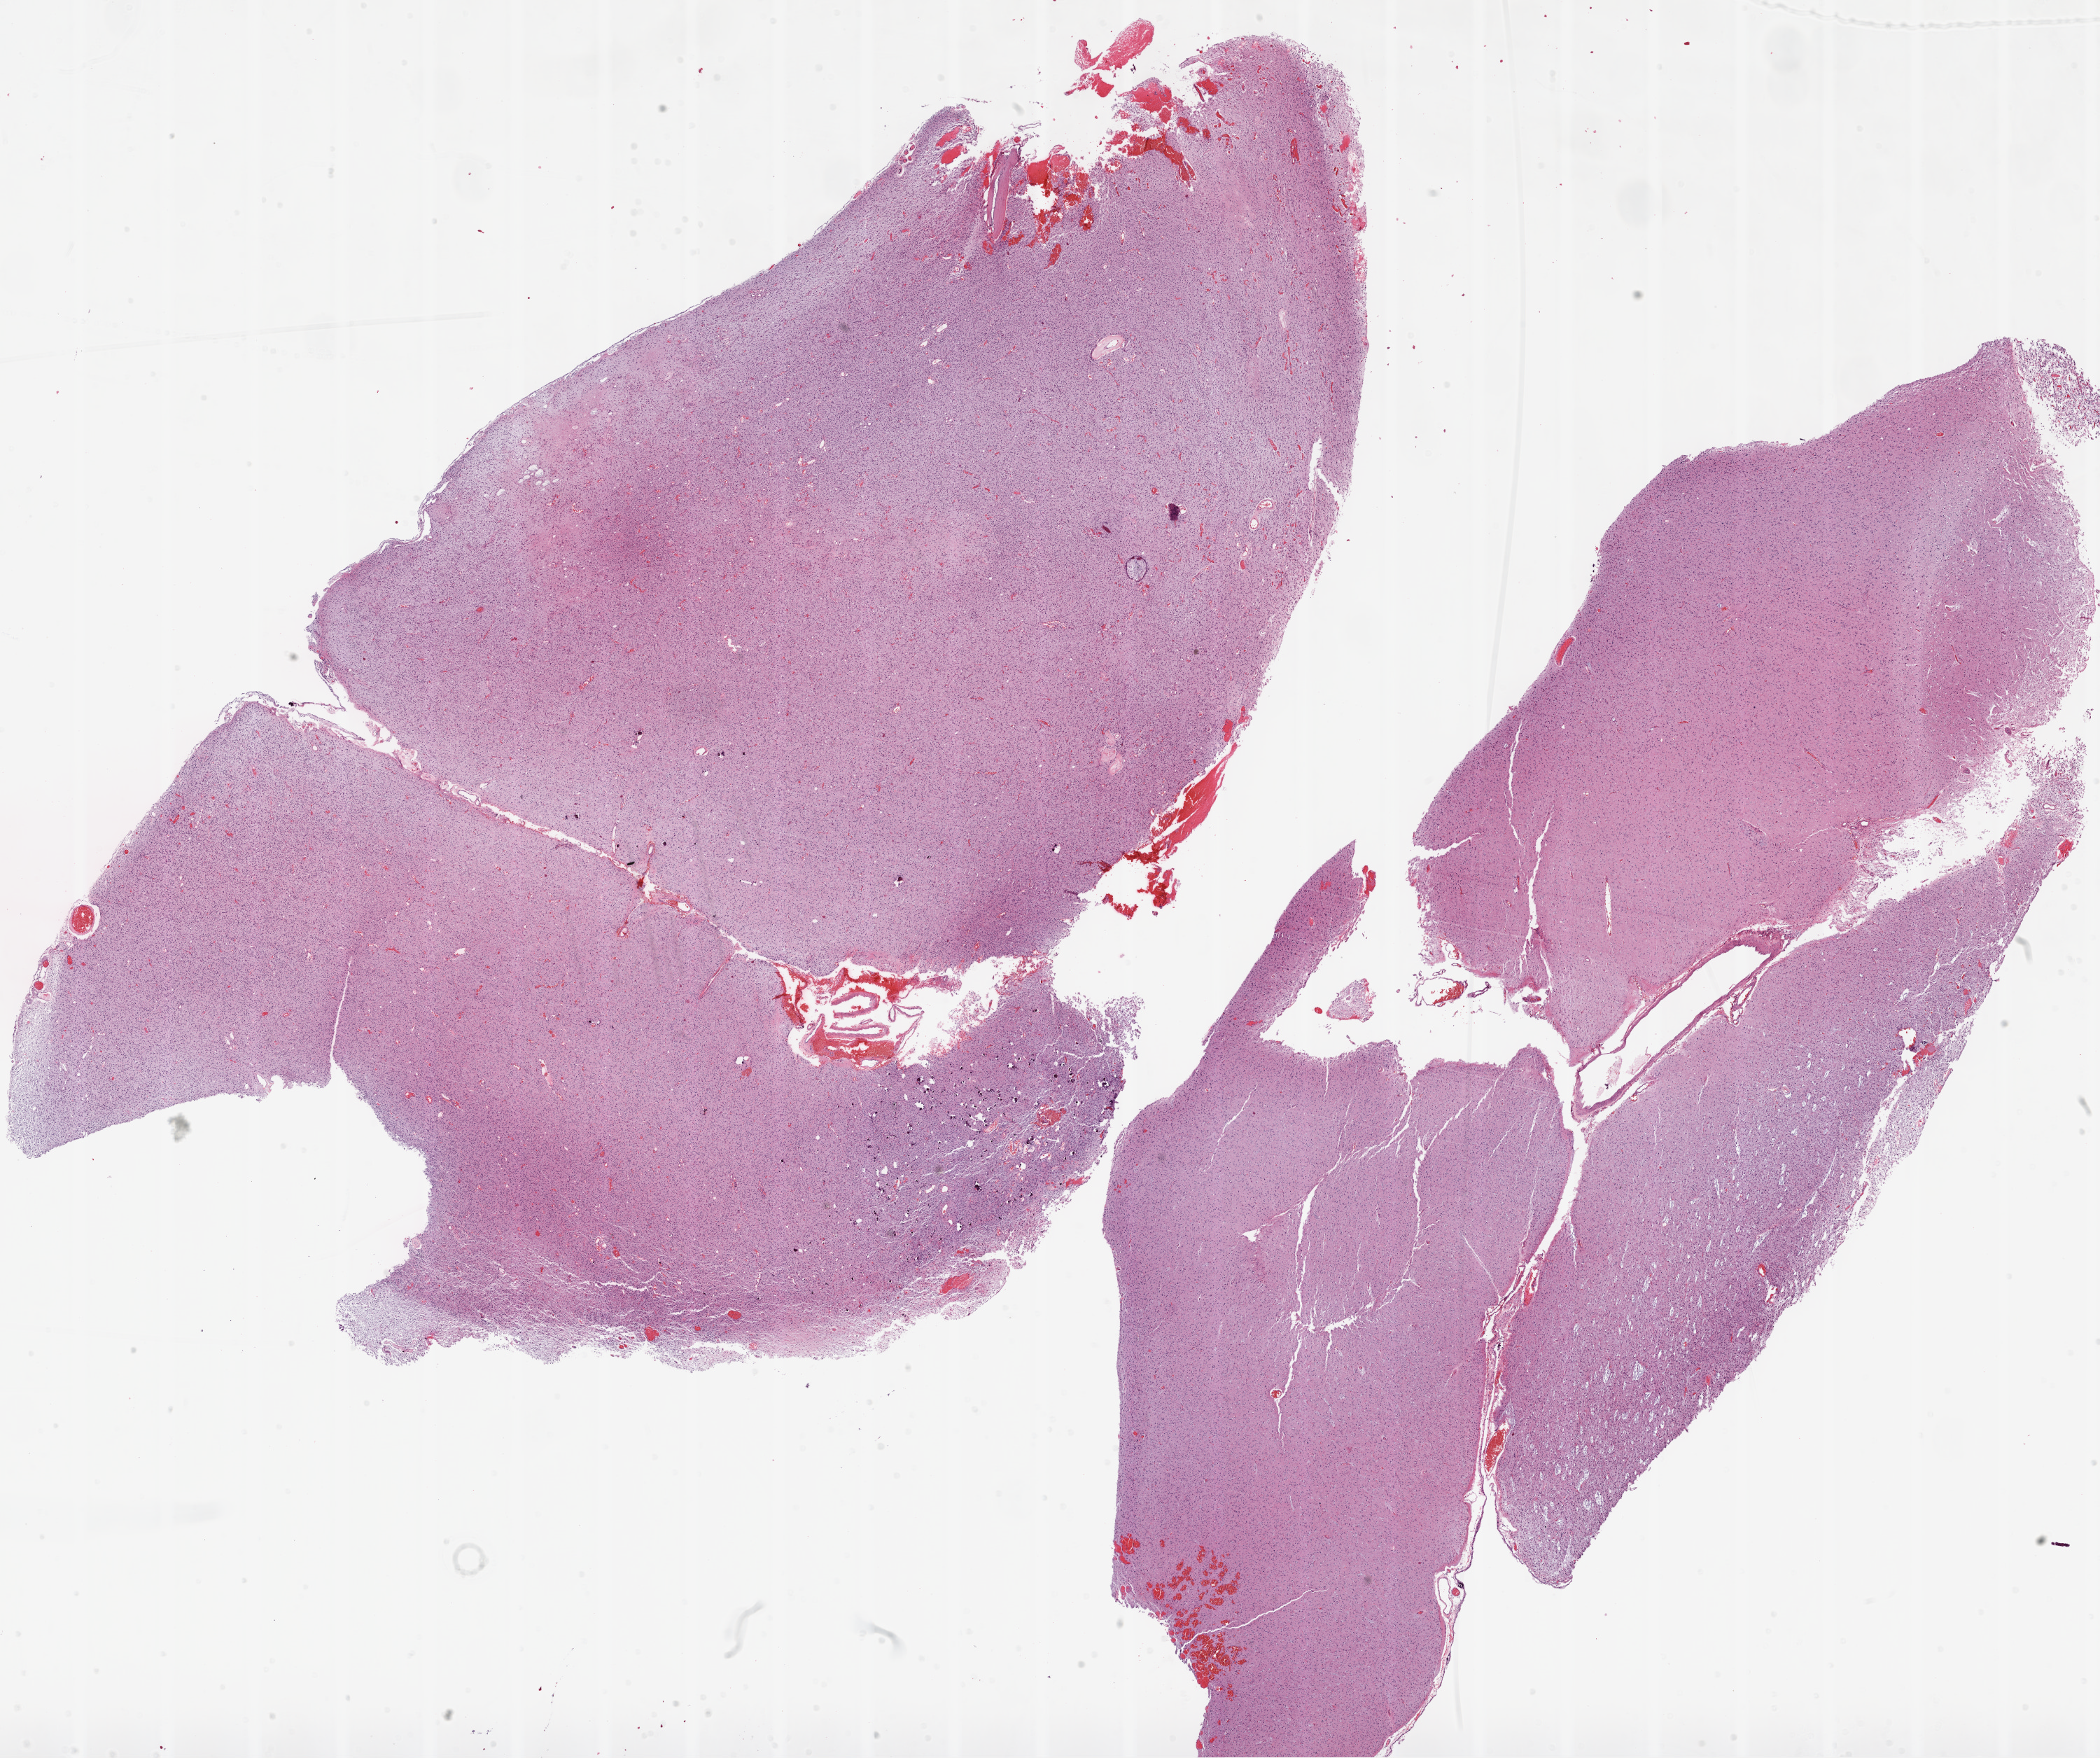
Hematoxylin and eosin (H&E) stained whole-slide image, whole scanned area (about 24.1 x 20.1 mm, from a 20x scan) shown as a low-resolution overview; FFPE section; primary tumour sample from the brain. Male patient; age at initial diagnosis 54 years.
Histologic diagnosis: Glioblastoma.